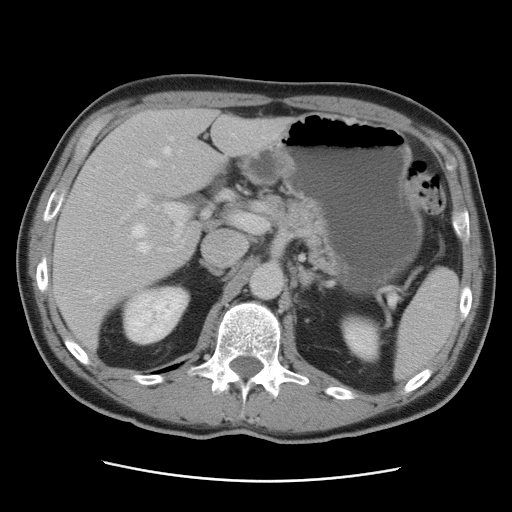
Contrast-enhanced abdominal CT, one axial slice; position 54 of 89 along the scan axis; 120 kVp; intravenous contrast given; soft-tissue window (W 400 / L 40 HU); 5 mm slice thickness; 512 × 512 image matrix, field of view 366 × 366 mm. Male patient, age 59 years. From the clinical record (not read from this slice): diagnosis: colorectal cancer liver metastases, imaged before liver resection; multiple liver metastases: yes; largest metastasis: 0.6 cm.
Annotated regions visible in this slice (outlined manually by an expert reader):
- hepatic veins: bounding box <83,133,238,303> (left, top, right, bottom; pixels)
- liver: <53,109,292,353>
- planned liver remnant (the part of the liver to remain after resection): <72,109,226,239>
- portal vein (with intrahepatic branches): <135,194,263,252>